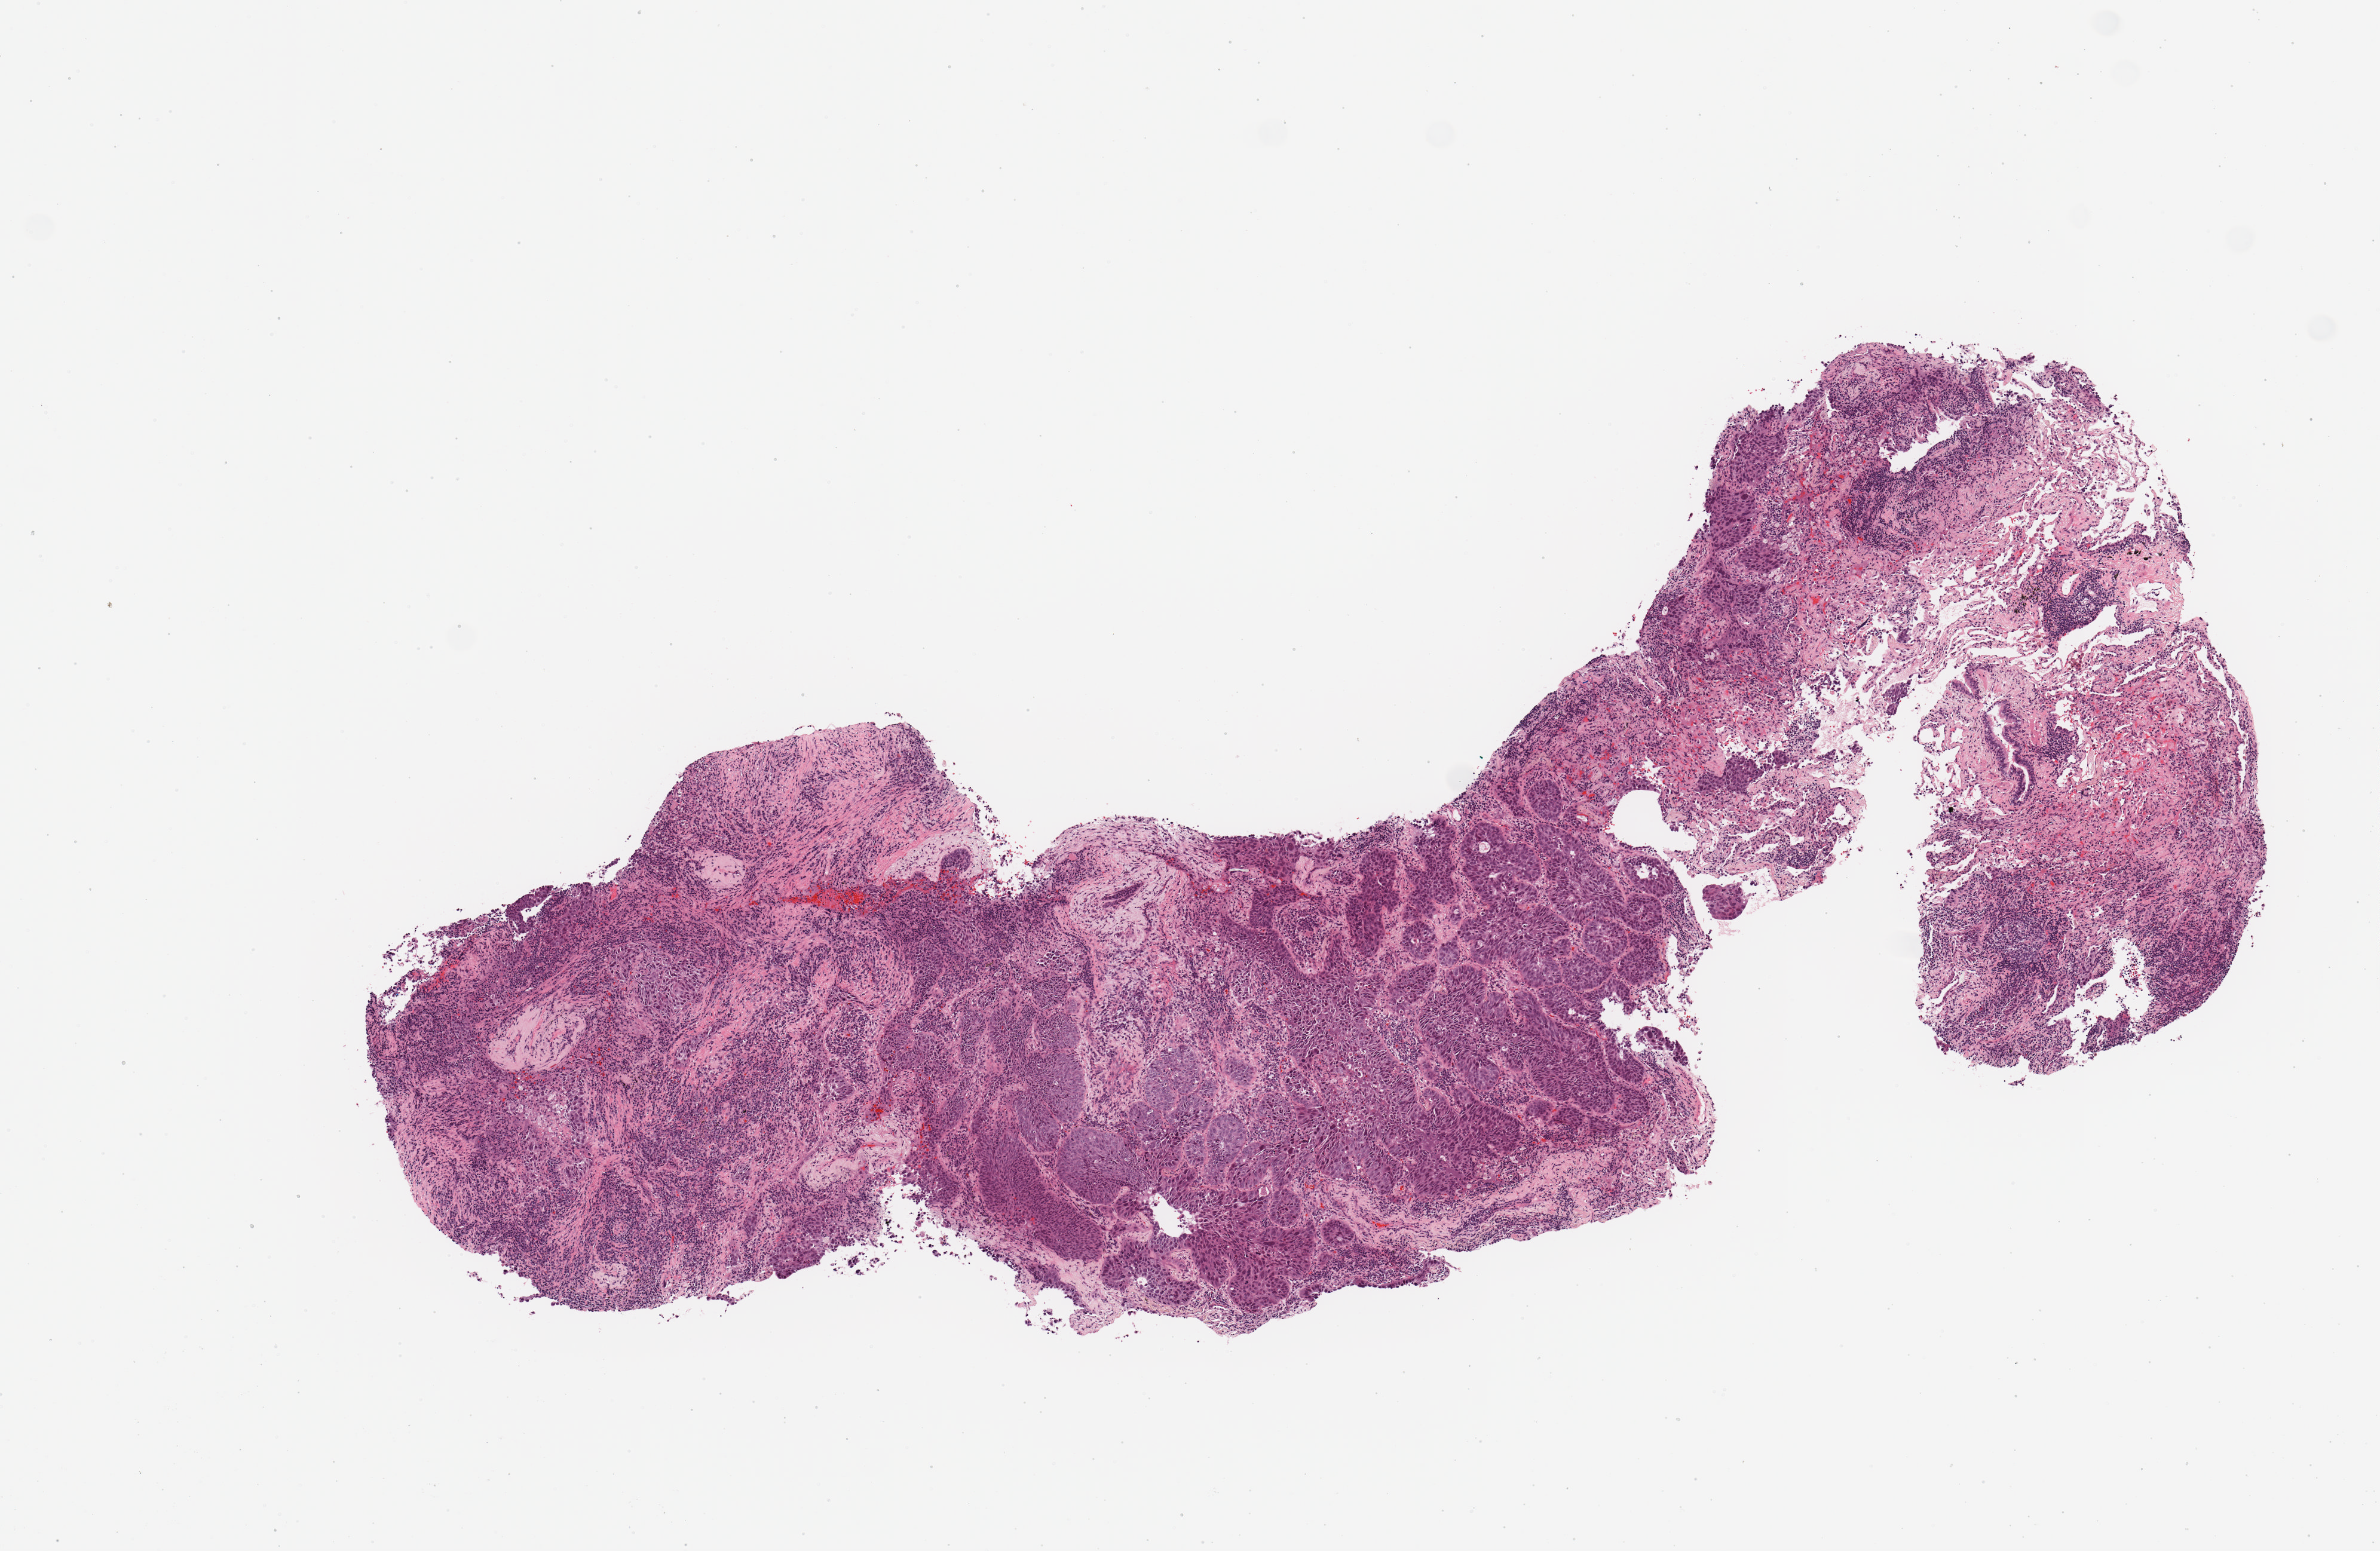
Whole-slide histology image, Hematoxylin and eosin (H&E) stained, shown as a low-resolution overview of the whole scanned area (about 7.9 x 5.1 mm, acquisition: 20x scan); tumour tissue sample, sampled site: lung. Patient: female, age 66 years. Histologic grade: G3 (poorly differentiated). Pathologist review of this section (percent, as recorded): tumour nuclei 65%, necrosis 5%.
Diagnosis: Squamous cell carcinoma, NOS. AJCC pathologic stage: IIB.